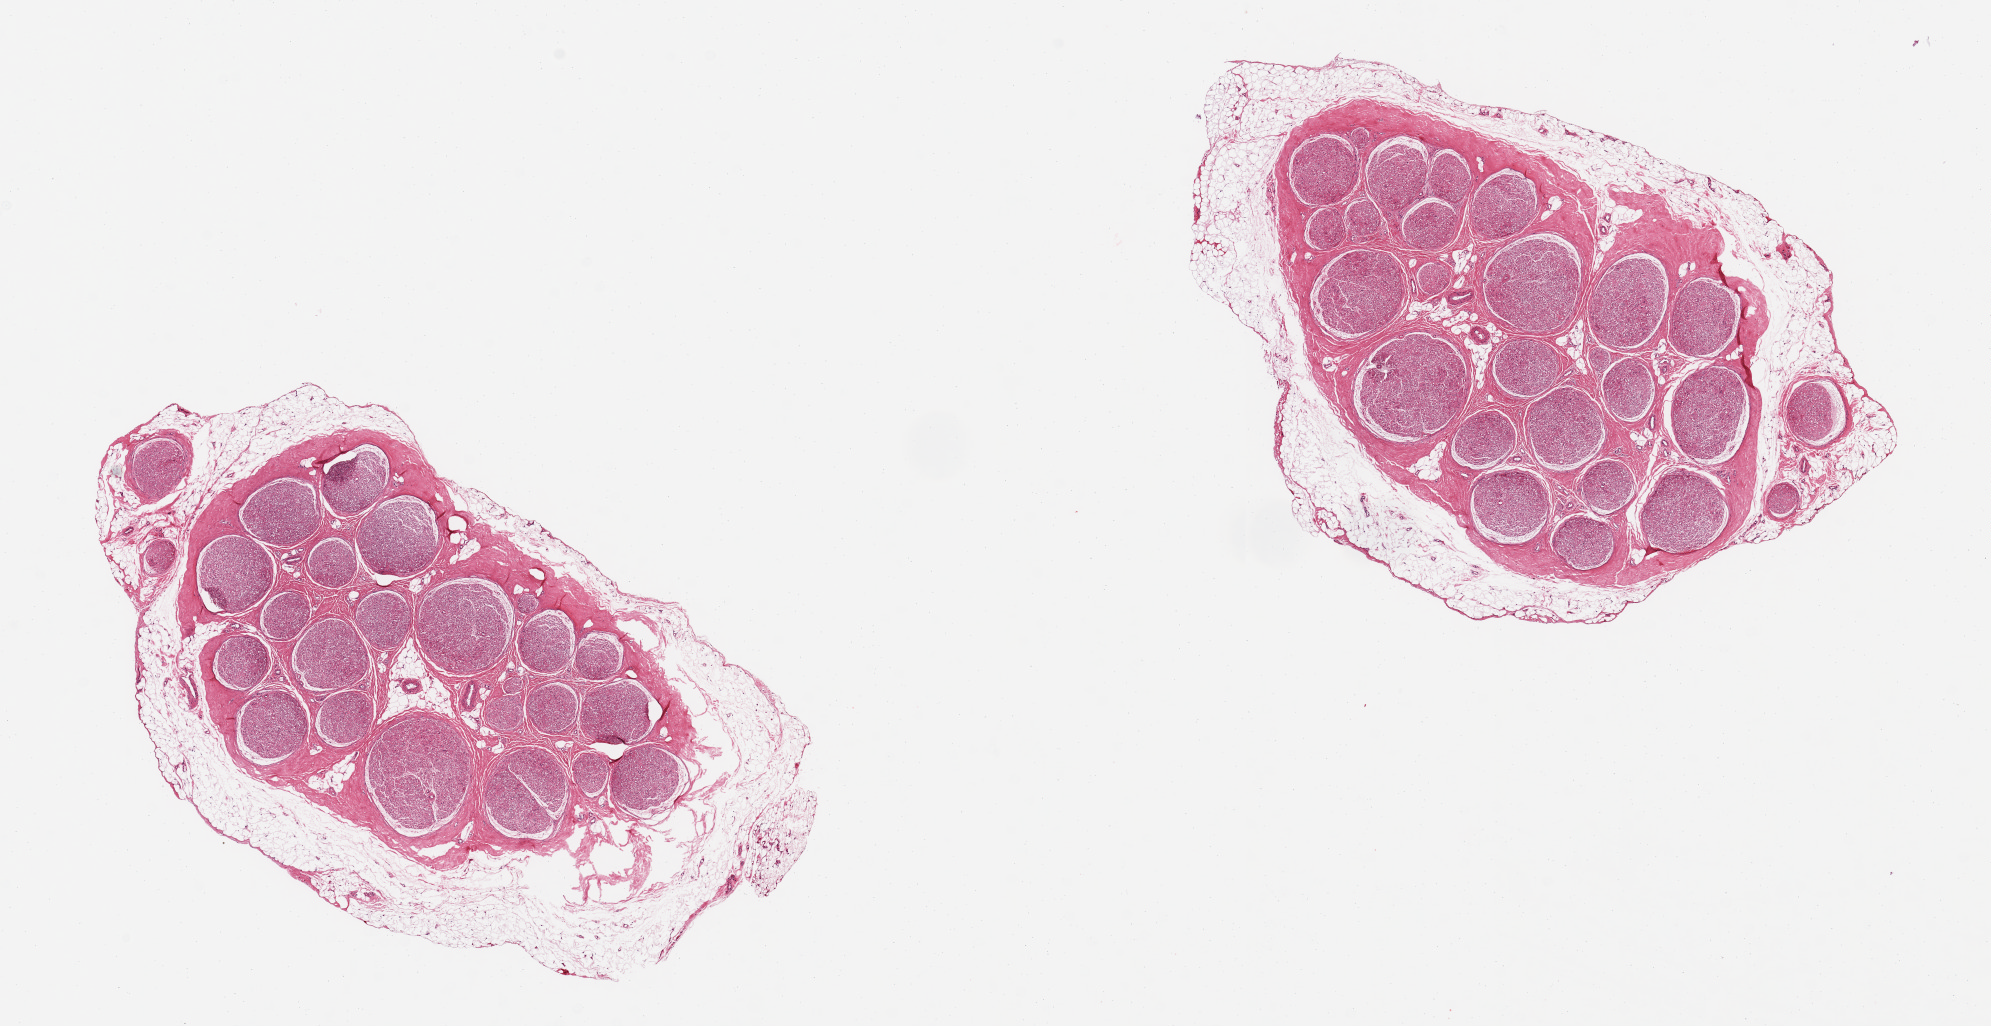
Digitized hematoxylin and eosin (H&E)-stained section, whole scanned area (about 15.8 x 8.1 mm, from a 20x scan) shown as a low-resolution overview; PAXgene-fixed paraffin-embedded (PFPE) section; target tissue: tibial nerve; donor tissue sample. Male donor.
Pathologist's review note for this sample: 2 pieces 5x3 & 5x4 mm; ~30% adipose circular envelope between 0.5 and 1.0 mm thick (could be trimmed).